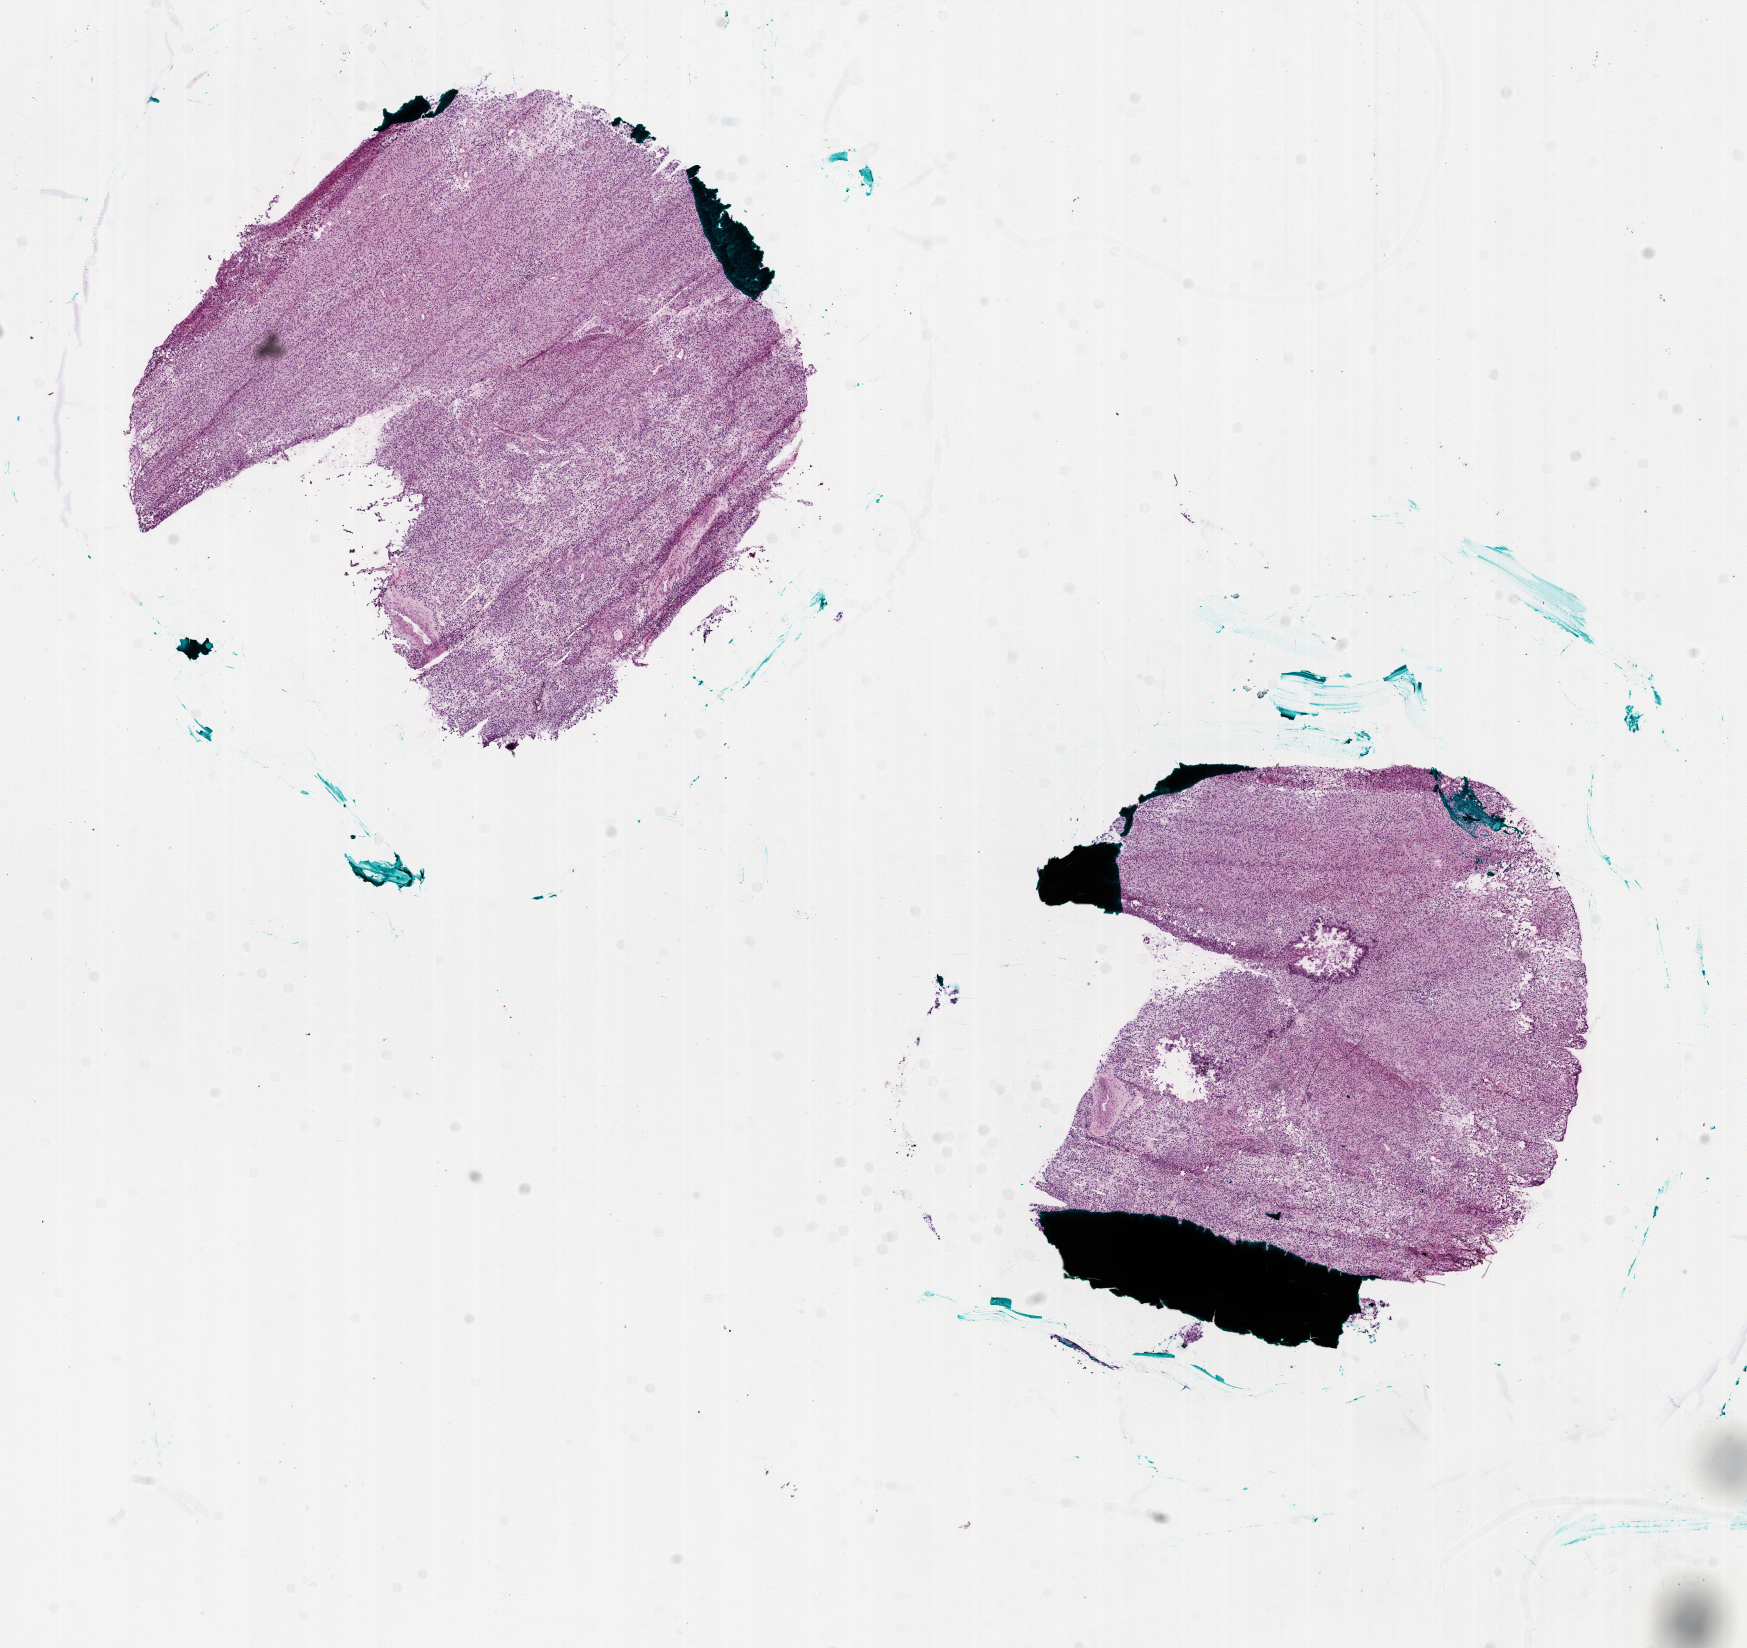
Whole-slide histology image, Hematoxylin and eosin (H&E) stained, low-resolution overview of the scanned area, about 14.0 x 13.2 mm (slide scanned at 20x), frozen section from the bottom of the tissue portion, sample: primary tumour, brain. Male patient; age at initial diagnosis 76 years.
Histologic diagnosis: Glioblastoma.